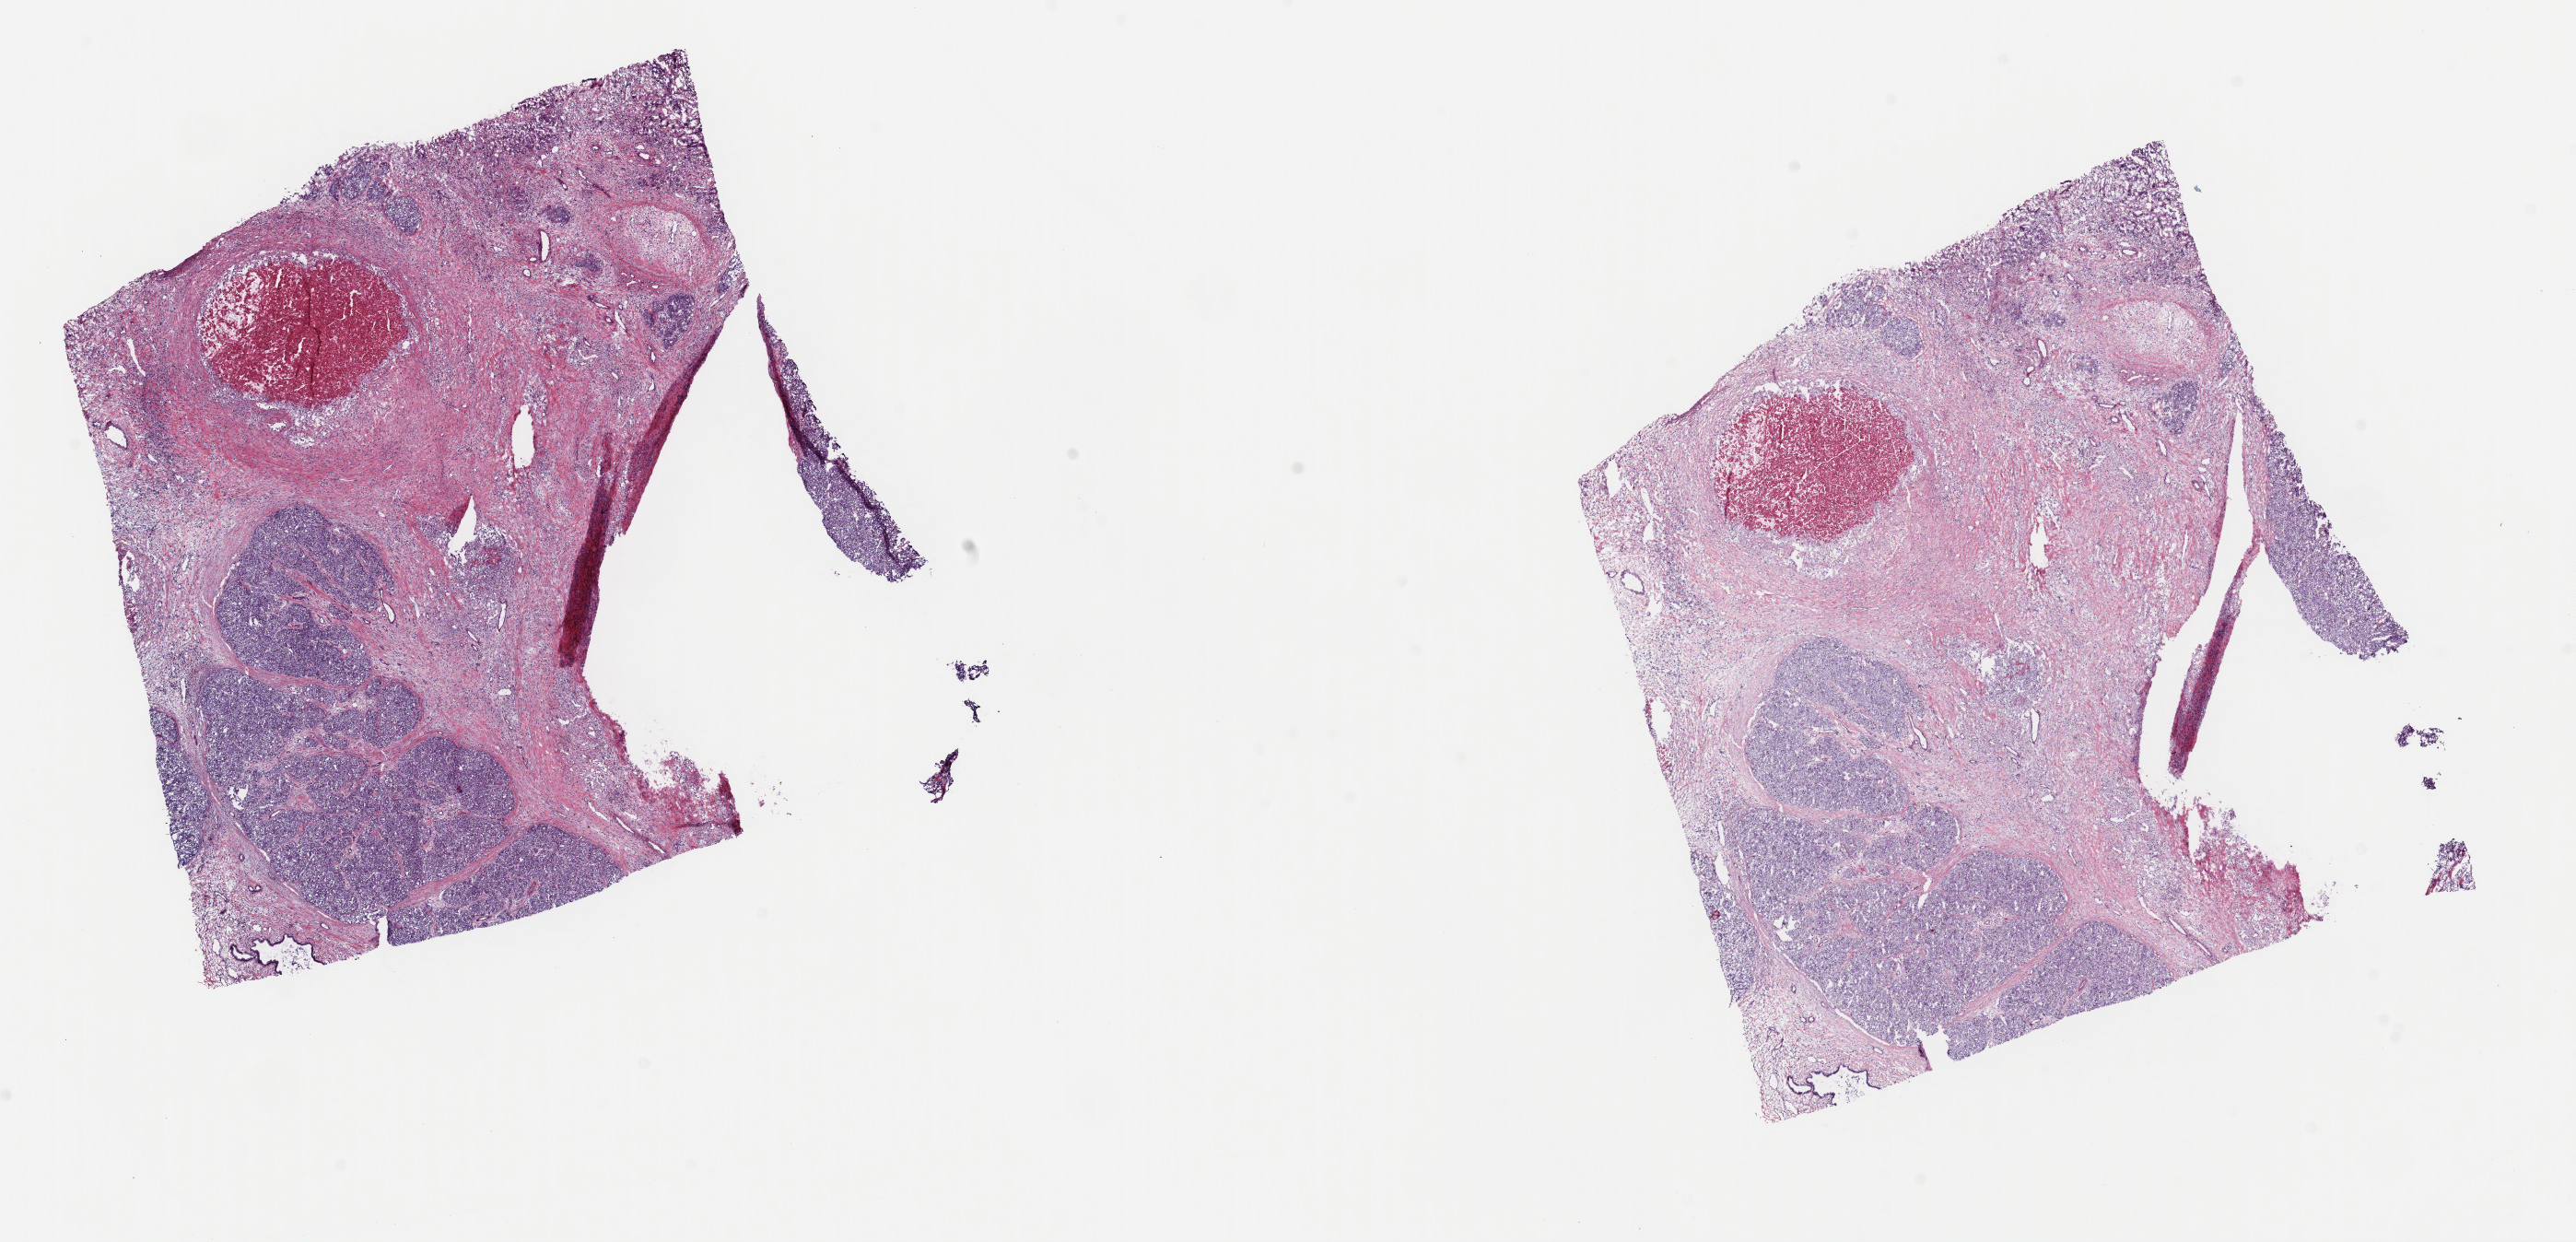
Digitized Hematoxylin and eosin (H&E) stained tissue section (whole slide) — whole scanned area (about 22.1 x 10.6 mm, slide scanned at 40x) shown as a low-resolution overview; frozen section from the top of the tissue portion; primary tumour sample from the liver. Male patient; age at initial diagnosis 35 years. Histologic grade: G3 (poorly differentiated). Pathologist review of this section (percent, as recorded): tumour cells 35%, tumour nuclei 80%, normal cells 0%, stromal cells 58%, necrosis 7%. Infiltration values recorded for this section: lymphocyte infiltration 5%, monocyte infiltration 4%, neutrophil infiltration 0%.
AJCC pathologic stage: IIIA (7th edition). Histologic diagnosis: Hepatocellular carcinoma, NOS.